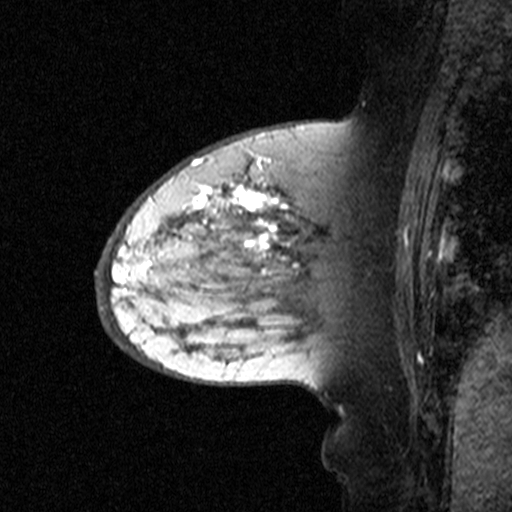
Breast MRI (dynamic contrast-enhanced), one sagittal slice. Slice 19 of 44 in the series (ordered by position). Dynamic contrast-enhanced study with each time point stored as its own series, time point 2 of 3 at this slice position (early post-contrast, ordered by acquisition time). 1.5 T. TE 4.5 ms, TR 11 ms. 512 × 512 image matrix, field of view 200 × 200 mm. Female patient, age 65 years. From the clinical record (not read from this slice): setting: breast cancer imaged before/during neoadjuvant chemotherapy; receptor status: HER2-positive.
Structures marked on this image (semi-automatic segmentation, software-assisted and operator-edited):
- analysis volume of interest (the breast-tissue region the enhancement analysis was run in; not a lesion): bounding box (x1, y1, x2, y2) in pixels: (160, 172, 329, 345)
- tumour enhancement mask (voxels above the 90 % enhancement threshold inside the analysis volume of interest): (175, 172, 298, 266)